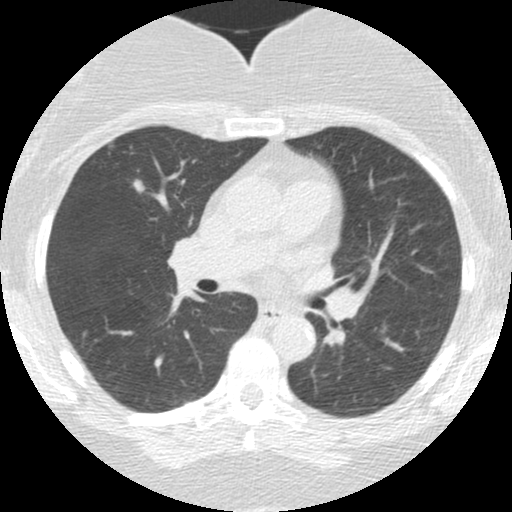
Low-dose screening chest CT, one axial slice. Slice 95 of 150 in the series (ordered by position). 120 kVp. Lung window (W 1500 / L -600 HU). 2.5 mm slice thickness. 512 × 512 image matrix, field of view 286 × 286 mm.
Outlined on this slice (outlined manually by an expert reader):
- lesion 1 (tumor, upper lobe of right lung): box from (x=132, y=179) to (x=146, y=193) px